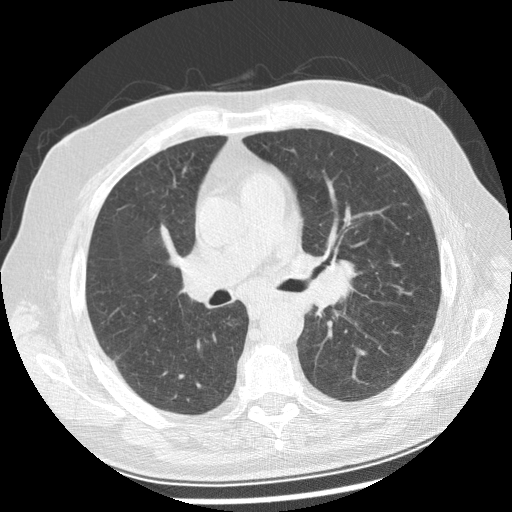
Chest CT (low-dose screening protocol), one axial image; first (baseline) screen; lung window (W 1500 / L -600 HU); 2.5 mm slice thickness; standard (soft-tissue) reconstruction kernel (STANDARD); 120 kVp; slice 106 of 250 in the series. Male, age 70 years at enrolment. Current smoker at enrolment.
Lesion marked by an expert reader, box from (x=283, y=242) to (x=365, y=312) px. Screening reader's record for this exam: no non-calcified nodule ≥4 mm recorded.